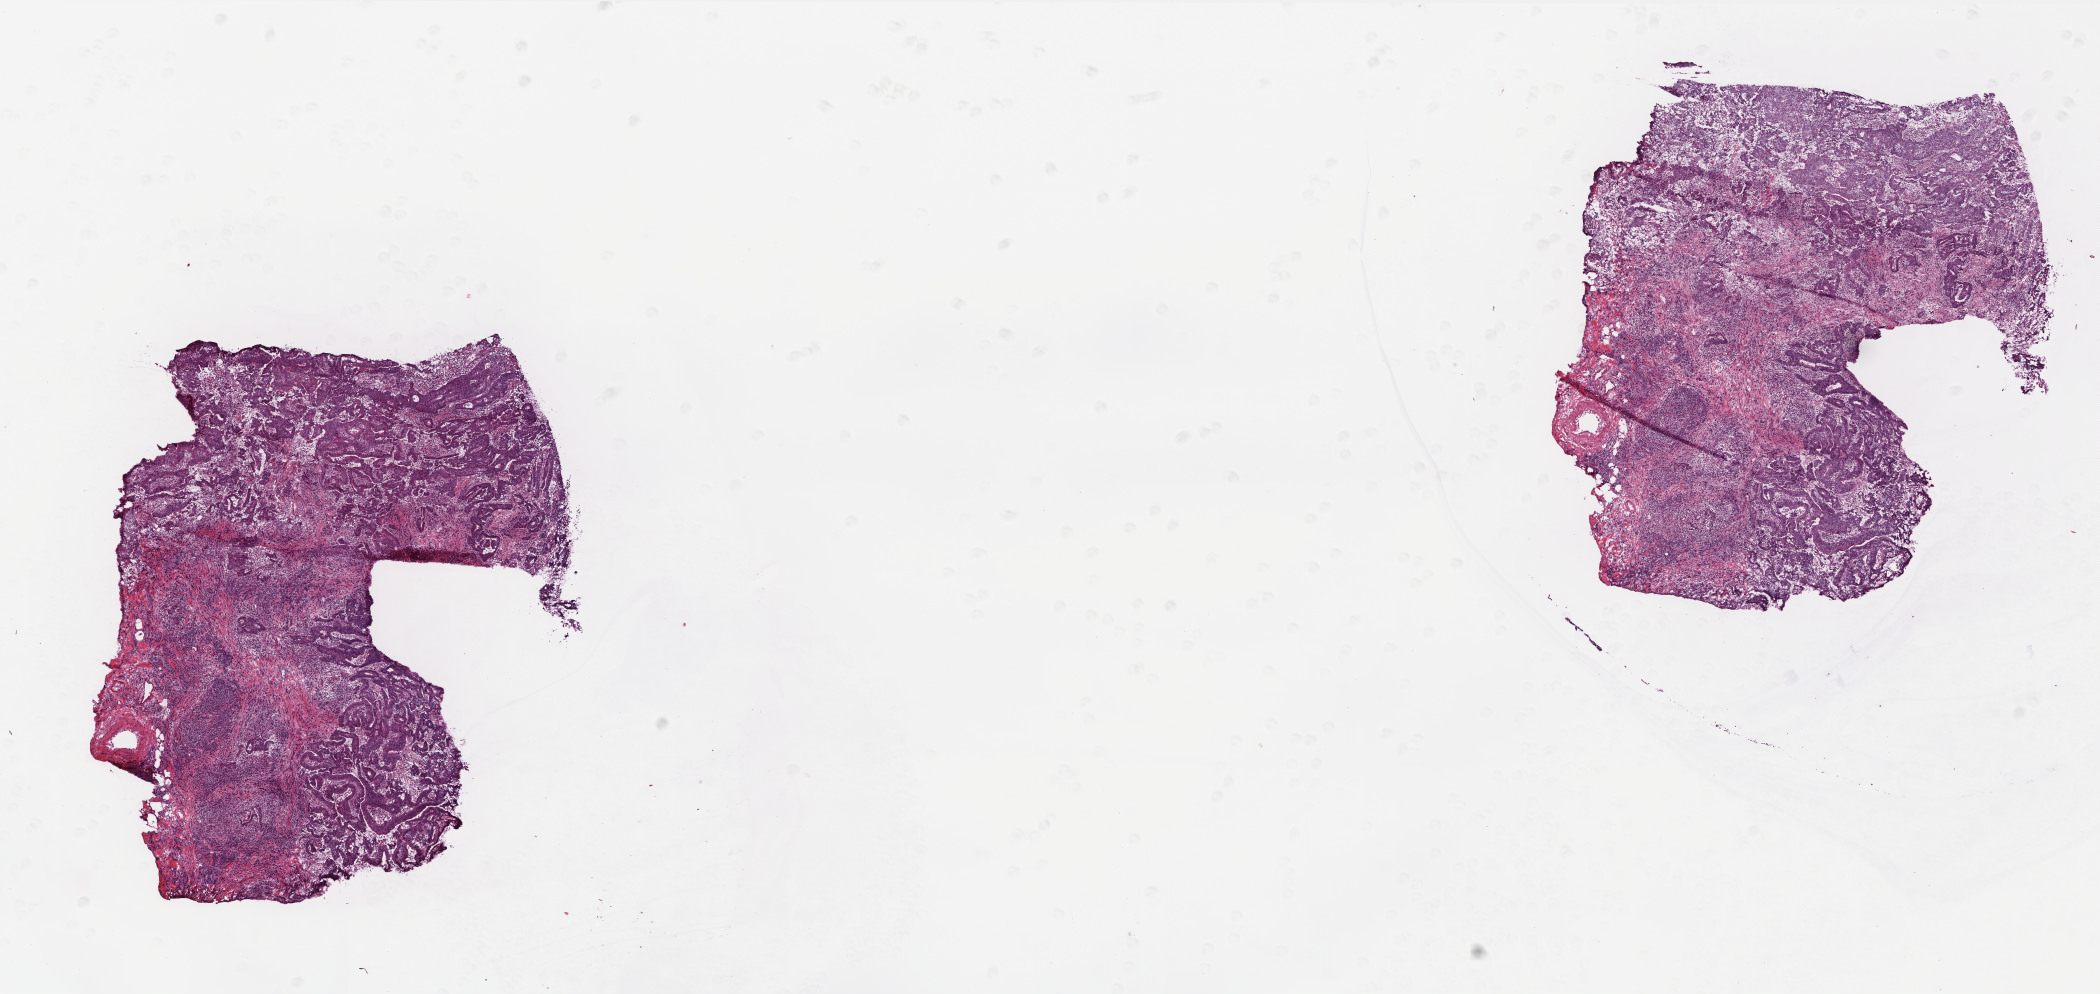
H&E-stained whole-slide image — low-resolution overview of the scanned area, about 16.8 x 8.0 mm, frozen section, colon, primary tumour sample. Male patient; age at initial diagnosis 70 years. Composition of this section per pathologist review: tumour cells 75%, tumour nuclei 60%, normal cells 0%, stromal cells 24%, necrosis 1%. Inflammatory infiltration, as recorded: lymphocyte infiltration 10%, monocyte infiltration 3%, neutrophil infiltration 20%.
Lymph nodes positive (case pathology): 0 of 28 examined. Histologic diagnosis: Adenocarcinoma, NOS (ascending colon). AJCC pathologic stage: I (6th edition).